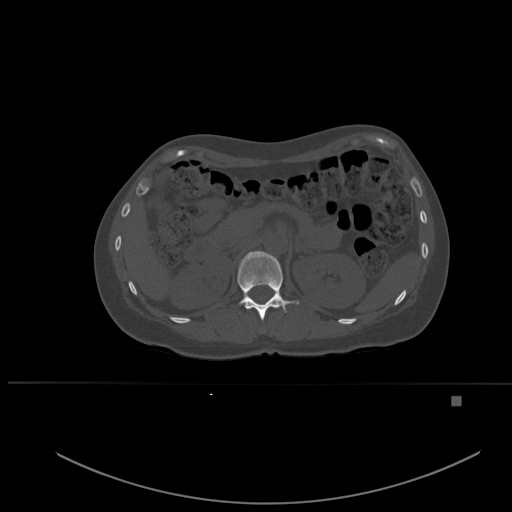
CT including the spine, one axial slice; slice 252 of 651 in the series (ordered by position); bone window (W 1800 / L 400 HU); 1.5 mm slice thickness; 512 × 512 image matrix. Female patient, age 49 years. Case-level facts recorded for this patient, not image findings: primary cancer: breast.
Structures marked on this image (semi-automatically segmented with operator editing):
- T12 vertebra: bounding box (x1, y1, x2, y2) in pixels: (237, 251, 299, 321)